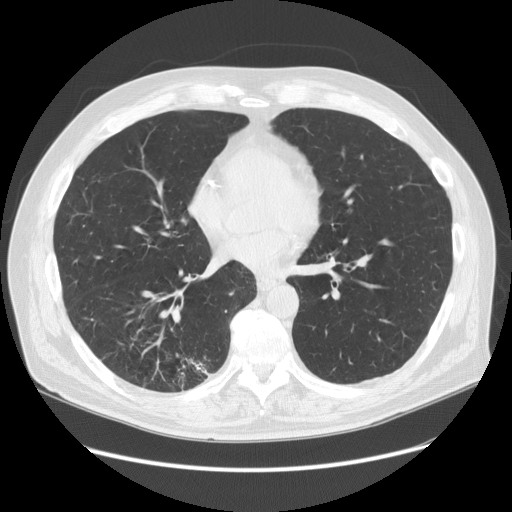
Axial slice from a low-dose chest CT screening exam; baseline annual screen; lung window (W 1500 / L -600 HU); slice 86 of 149 in the series; 512 × 512 image matrix, field of view 400 × 400 mm. Male, age 68 years at enrolment. Former smoker at enrolment.
Expert reader's lesion annotation, bounding box [x1, y1, x2, y2] px = [121, 329, 226, 405]. The exam's reader record, not a measurement of the box and not confirmed to be the same lesion: non-calcified nodule or mass ≥4 mm, right lower lobe, 37 × 20 mm, spiculated (stellate) margins, soft tissue attenuation. Lung cancer was diagnosed 24 days after this screen: adenosquamous carcinoma, right lower lobe, poorly differentiated (G3), stage IIIA (AJCC 6th edition), 30 mm at pathology.